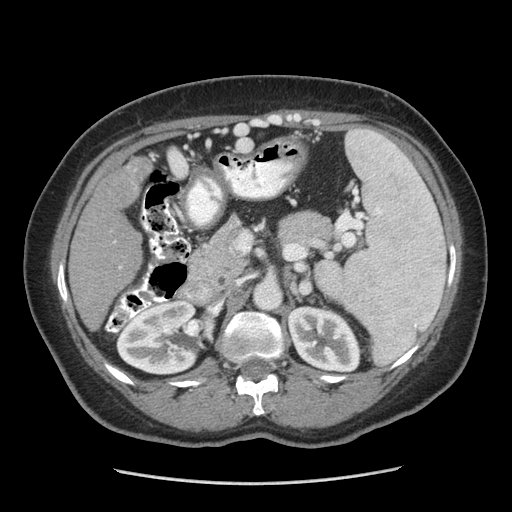
Contrast-enhanced abdominal CT (liver protocol), one axial slice. Slice 139 of 185 in the series (ordered by position). Soft-tissue window (W 400 / L 40 HU). 2.5 mm slice thickness. 512 × 512 image matrix. From the clinical record (not read from this slice): diagnosis: hepatocellular carcinoma (patient treated with transarterial chemoembolisation; whether this scan precedes or follows treatment is not stated here); TNM stage (as recorded): Stage-I.
Structures marked on this image (semi-automatically segmented with operator editing):
- liver parenchyma outside the tumour (the mass and vessels are separate outlines, so this box may not span the whole liver): bounding box (x1, y1, x2, y2) in pixels: (68, 152, 156, 330)
- mass: (90, 158, 151, 217)